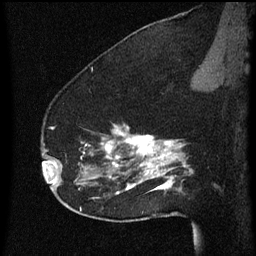
Breast MRI (dynamic contrast-enhanced), one sagittal slice. Position 43 of 60 along the scan axis. Dynamic contrast-enhanced series, image 2 of 3 at this slice position (ordered by acquisition). 1.5 T. TE 4.2 ms, TR 8 ms. 2 mm slice thickness. 256 × 256 image matrix. Female patient, age 52 years.
Outlined on this slice (semi-automatic segmentation, software-assisted and operator-edited):
- analysis volume of interest (the breast-tissue region the enhancement analysis was run in; not a lesion): bounding box <54,124,178,207> (left, top, right, bottom; pixels)
- tumour enhancement mask (voxels above the 70 % enhancement threshold inside the analysis volume of interest): <54,126,177,195>